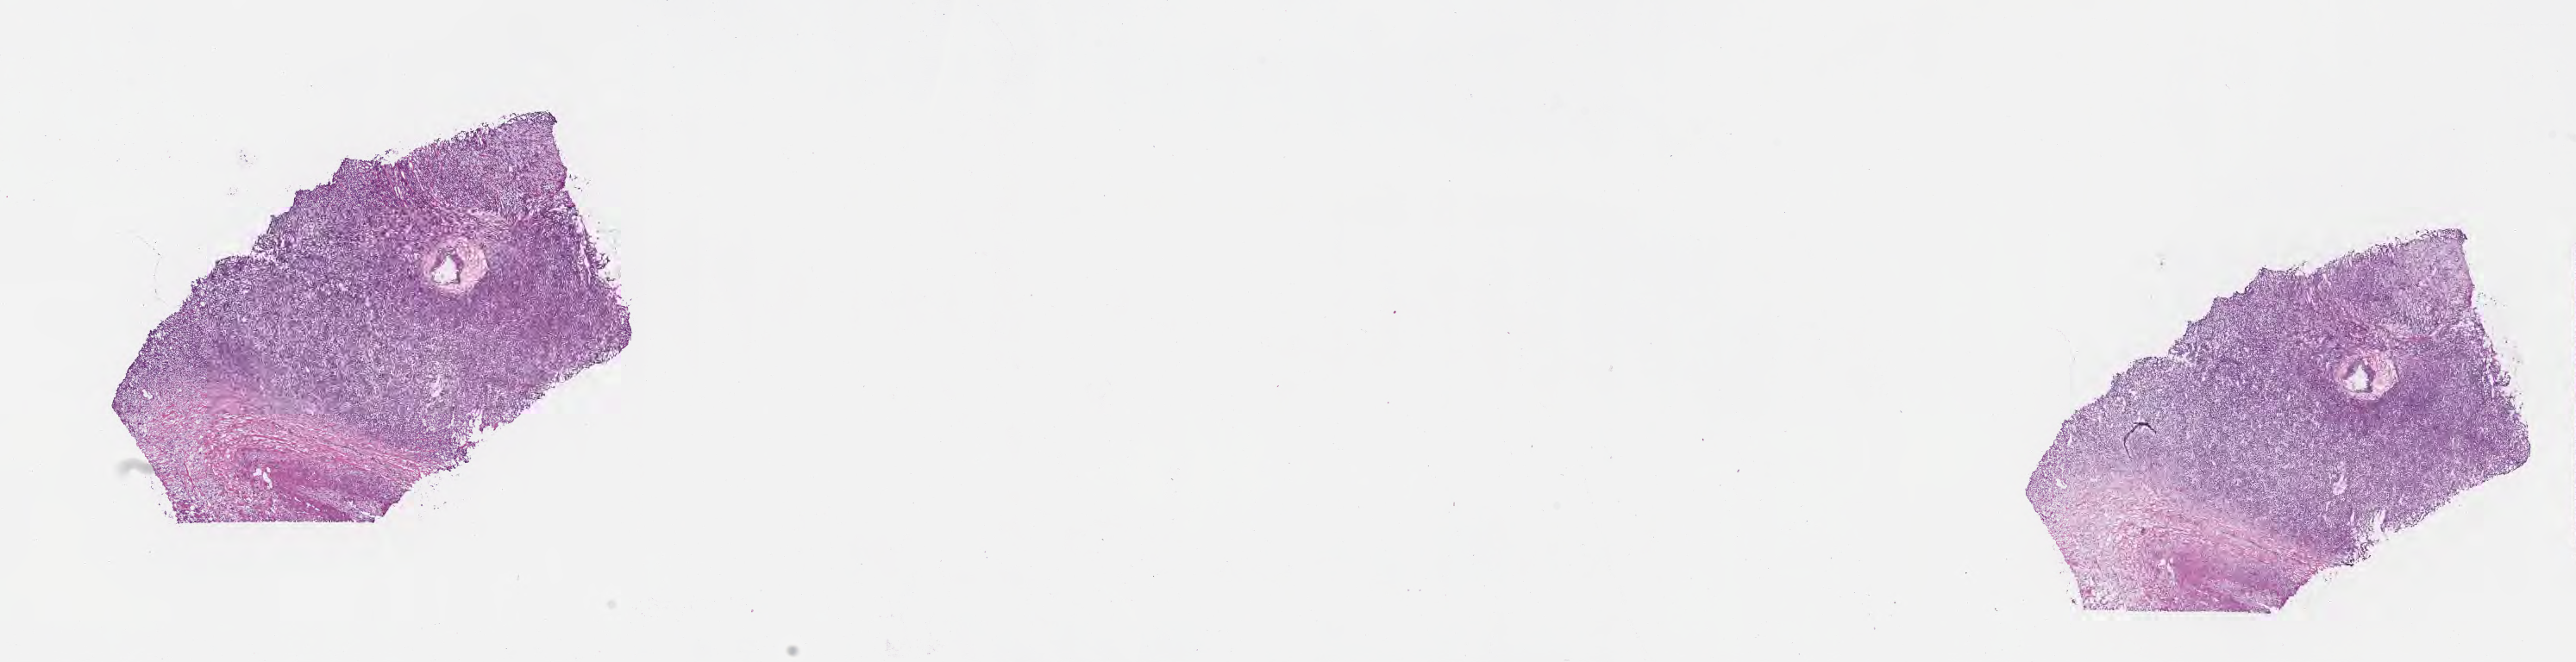
Hematoxylin and eosin (H&E) whole-slide image — shown as a low-resolution overview of the whole scanned area (about 24.2 x 6.2 mm), frozen section (tissue freezing medium), specimen: metastatic tumor tissue, resected from connective, subcutaneous and other soft tissues. Female patient; age at initial diagnosis 68 years. Pathologist review of this section (percent, as recorded): tumor cells 66%, tumor nuclei 90%, stromal cells 33%, necrosis 1%, normal cells 0%. Inflammatory infiltration, as recorded: lymphocyte infiltration 8%, monocyte infiltration 0%, neutrophil infiltration 0%.
Patient diagnosis (primary): Malignant melanoma, NOS. Section: bottom of the tissue portion.